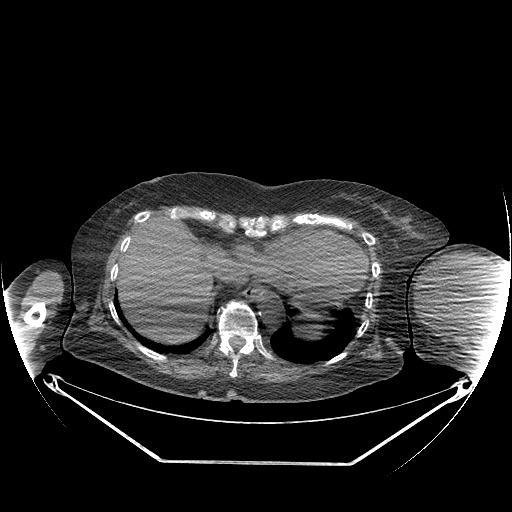
CT of an extremity soft-tissue mass (from a PET/CT study), one axial slice; slice 147 of 267 in the series (ordered by position); 140 kVp; soft-tissue window (W 400 / L 40 HU); 3.75 mm slice thickness; 512 × 512 image matrix. Female patient. From the clinical record (not read from this slice): histological type: pleiomorphic leiomyosarcoma; grade: high; site of the primary tumour: left biceps.
Outlined on this slice (expert contour drawn on MRI and transferred to this co-registered scan by the dataset authors):
- gross tumour volume including surrounding oedema: box from (x=420, y=253) to (x=499, y=325) px
- gross tumour volume (mass): (x=420, y=253)–(x=499, y=321)